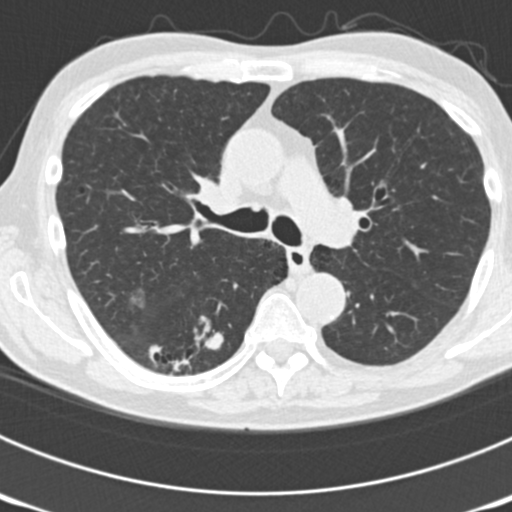
Low-dose screening chest CT, axial slice; third screening round (two years after baseline); lung window (W 1500 / L -600 HU); 120 kVp; slice 61 of 177 in the series. Male, age 70 years at enrolment. Current smoker at enrolment.
Expert-annotated lung lesion, box from (x=141, y=313) to (x=235, y=386) px. The screening reader recorded 3 non-calcified nodules or masses ≥4 mm on this exam; which of them this box marks is not recorded. Participant outcome: lung cancer diagnosed 14 days after this screen — bronchiolo-alveolar adenocarcinoma, NOS, right lower lobe, poorly differentiated (G3), stage IB (AJCC 6th edition), 30 mm at pathology.